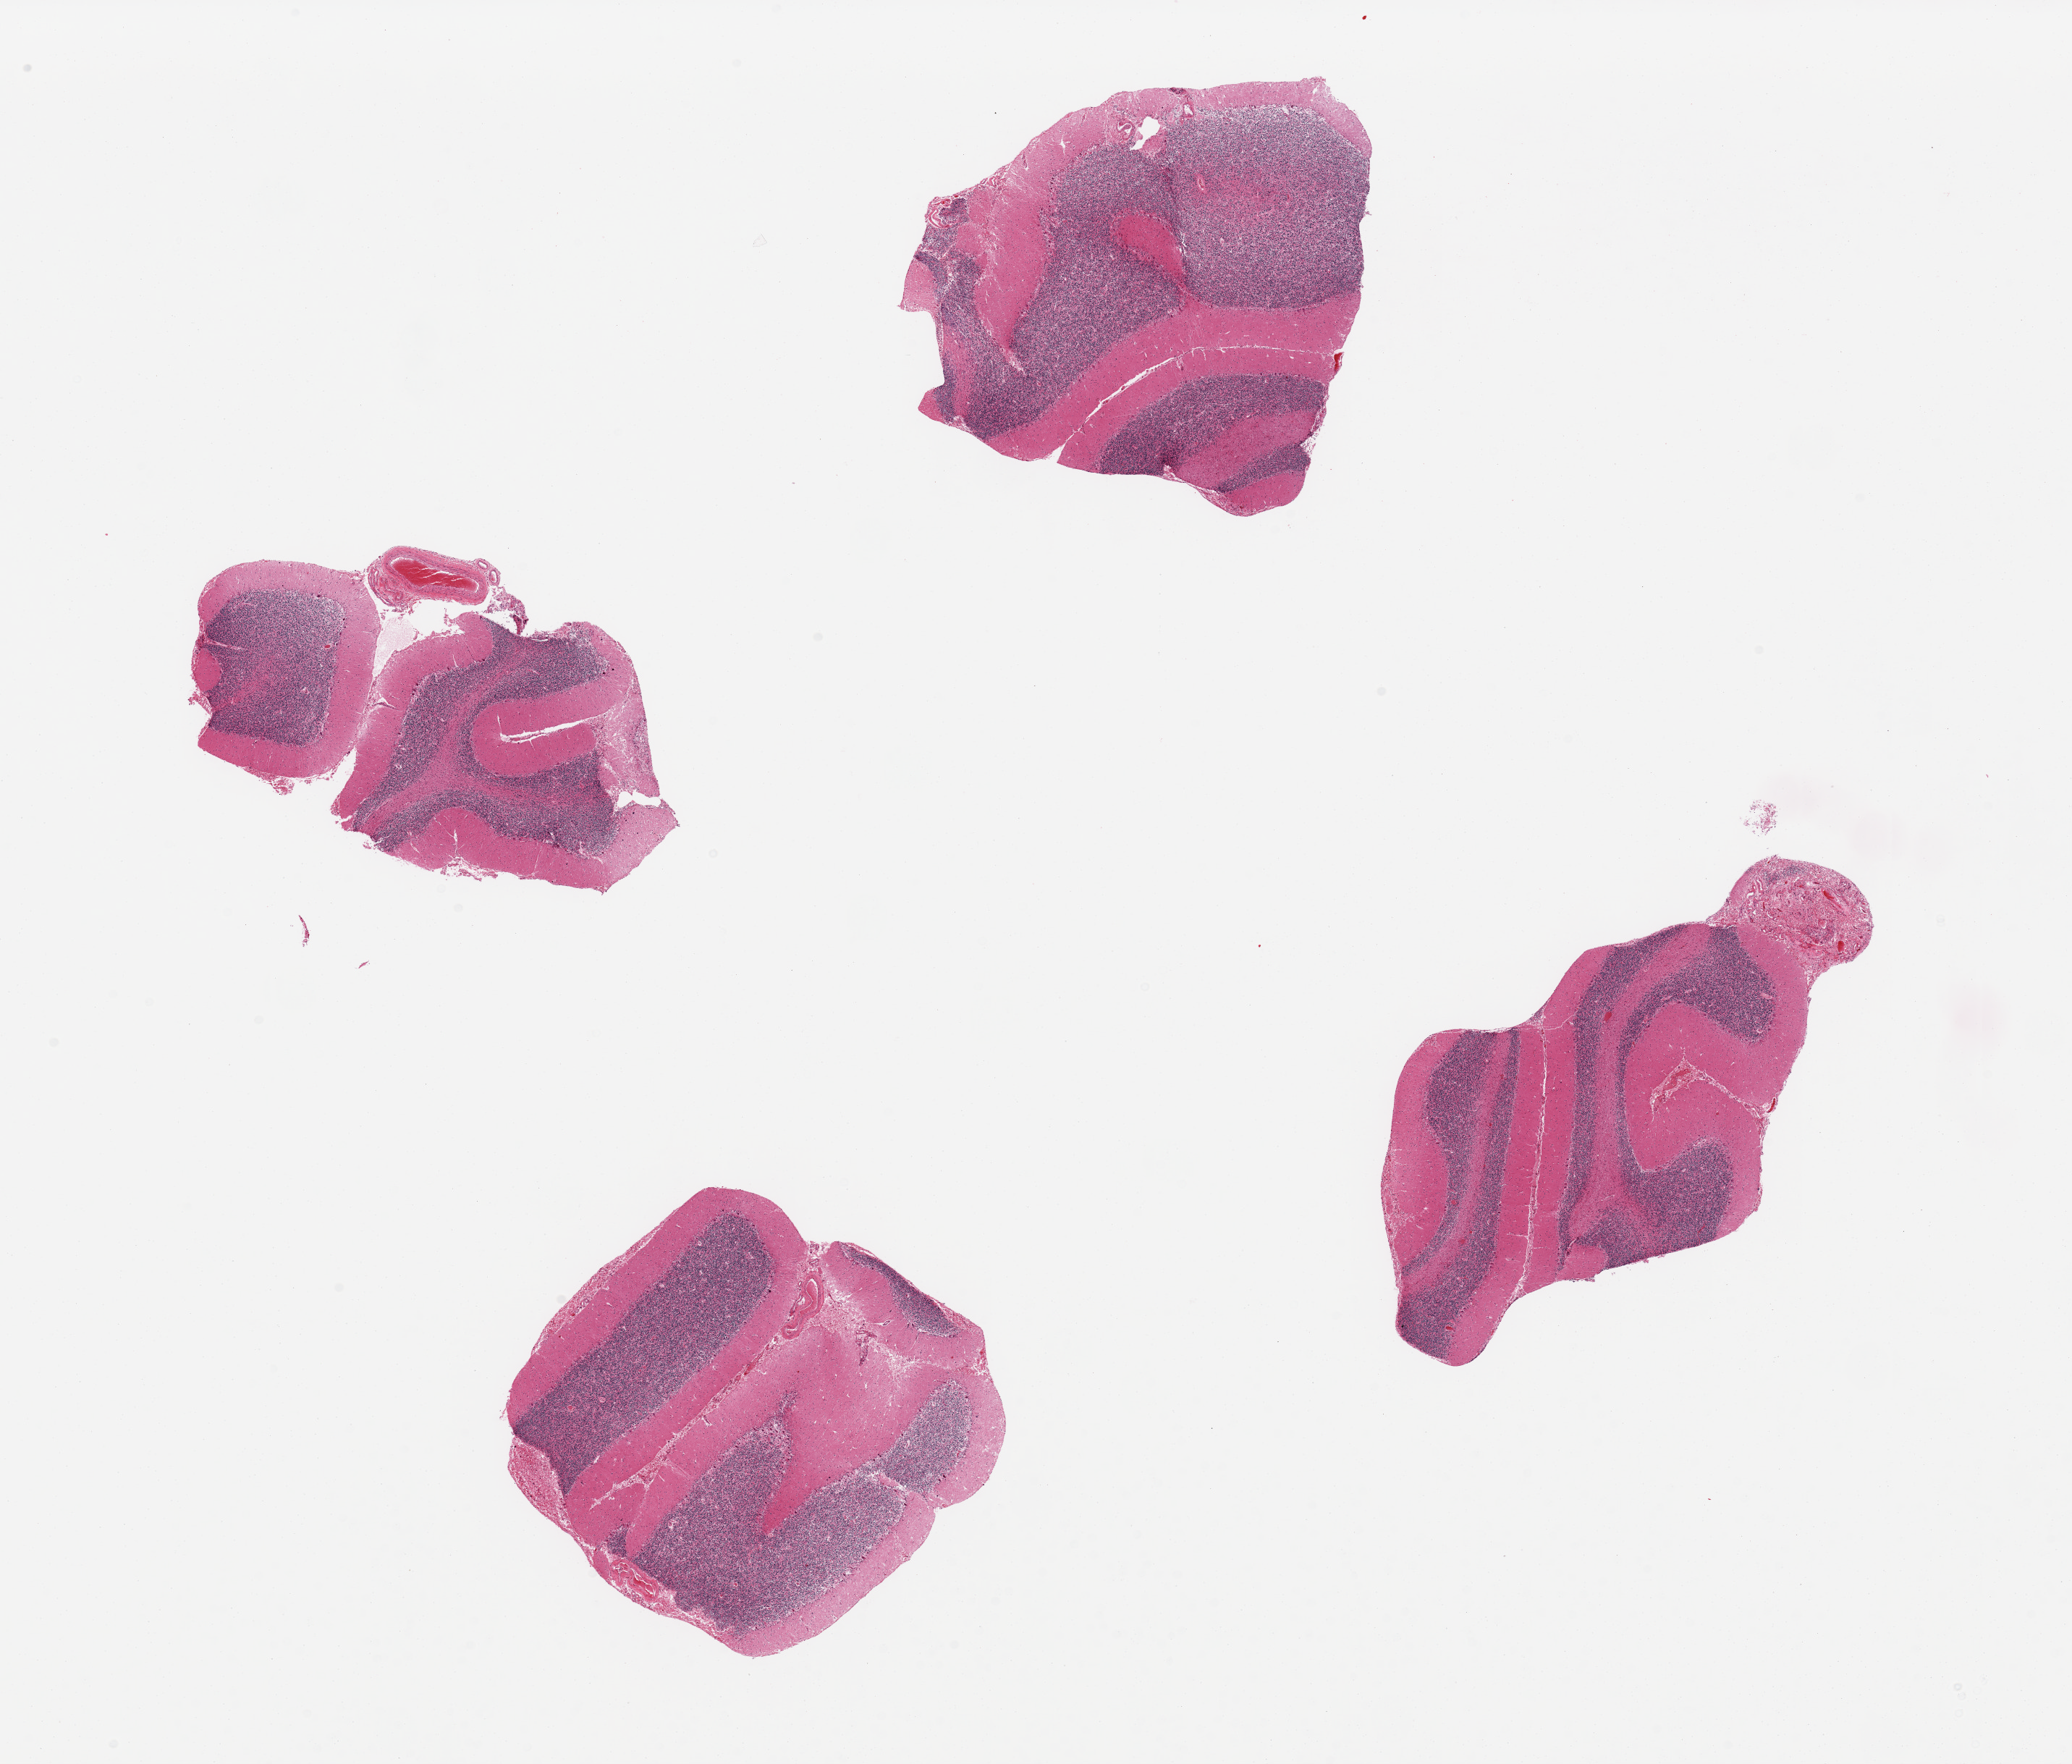
Digitized H&E-stained section — shown as a low-resolution overview of the whole scanned area (about 22.6 x 19.3 mm). PAXgene-fixed, paraffin-embedded tissue. Target tissue: cerebellum. Tissue donor sample.
• pathologist's review note for this sample: 4 pieces, Purkinje cells with some evidence of ischemic change